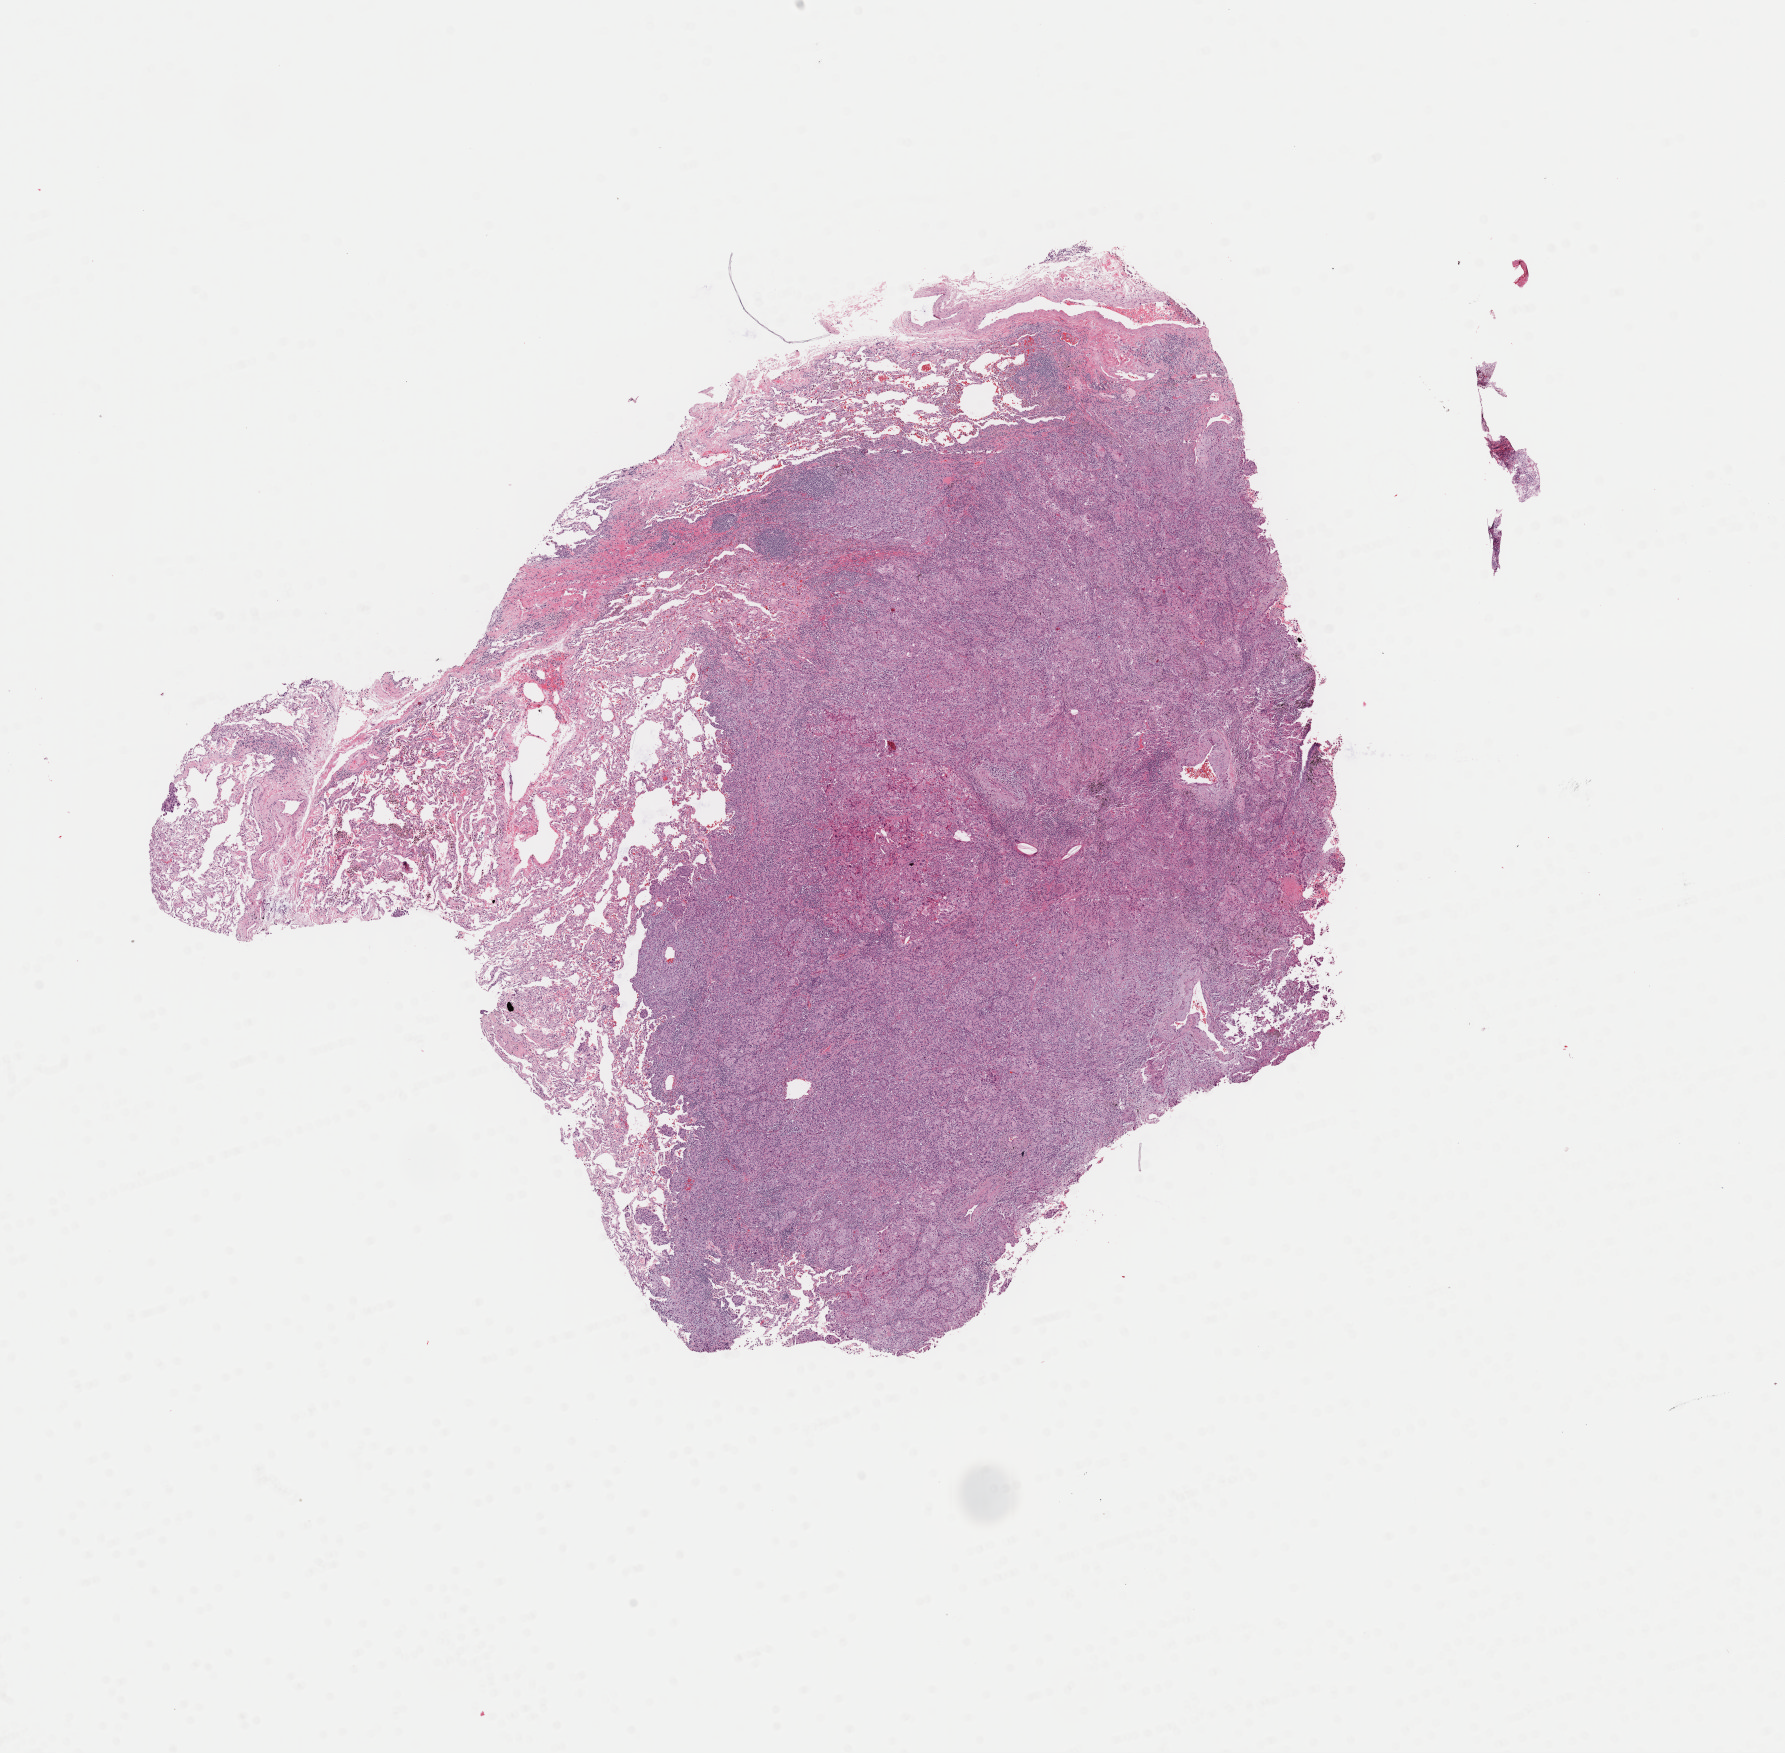
Hematoxylin and eosin (H&E) stained whole-slide image, low-resolution overview of the scanned area, about 14.1 x 13.8 mm. Frozen section. Lung, primary tumour sample. Male patient; age at initial diagnosis 59 years. Composition of this section per pathologist review: tumour cells 75%, tumour nuclei 75%, normal cells 2%, stromal cells 22%, necrosis 1%. Infiltration values recorded for this section: lymphocyte infiltration 5%, monocyte infiltration 2%, neutrophil infiltration 3%.
• AJCC pathologic stage: IB (6th edition)
• pathologic diagnosis: Adenocarcinoma, NOS (upper lobe, lung)